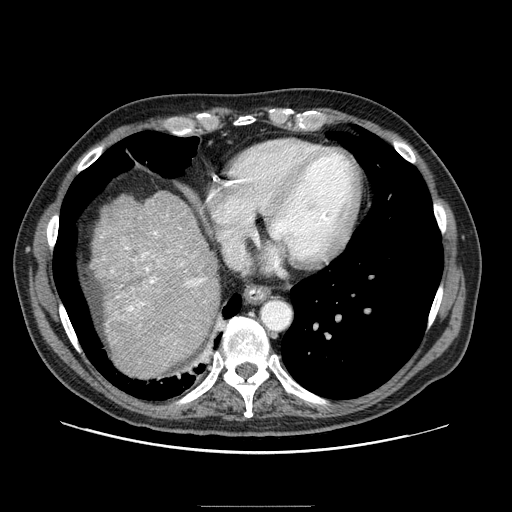
Contrast-enhanced abdominal CT (liver protocol), one axial slice; position 79 of 99 along the scan axis; reconstruction kernel STANDARD; one of 2 acquisitions stored at this slice position; soft-tissue window (W 400 / L 40 HU); 2.5 mm slice thickness; 512 × 512 image matrix. From the clinical record (not read from this slice): diagnosis: hepatocellular carcinoma (patient treated with transarterial chemoembolisation; whether this scan precedes or follows treatment is not stated here); TNM stage (as recorded): Stage-II; Child-Pugh class: A; tumour differentiation: well differentiated; tumour nodularity: multinodular.
Annotated regions visible in this slice (semi-automatically segmented with operator editing):
- liver parenchyma outside the tumour (the mass and vessels are separate outlines, so this box may not span the whole liver): bounding box <92,192,220,377> (left, top, right, bottom; pixels)
- liver vessels: <111,231,206,318>